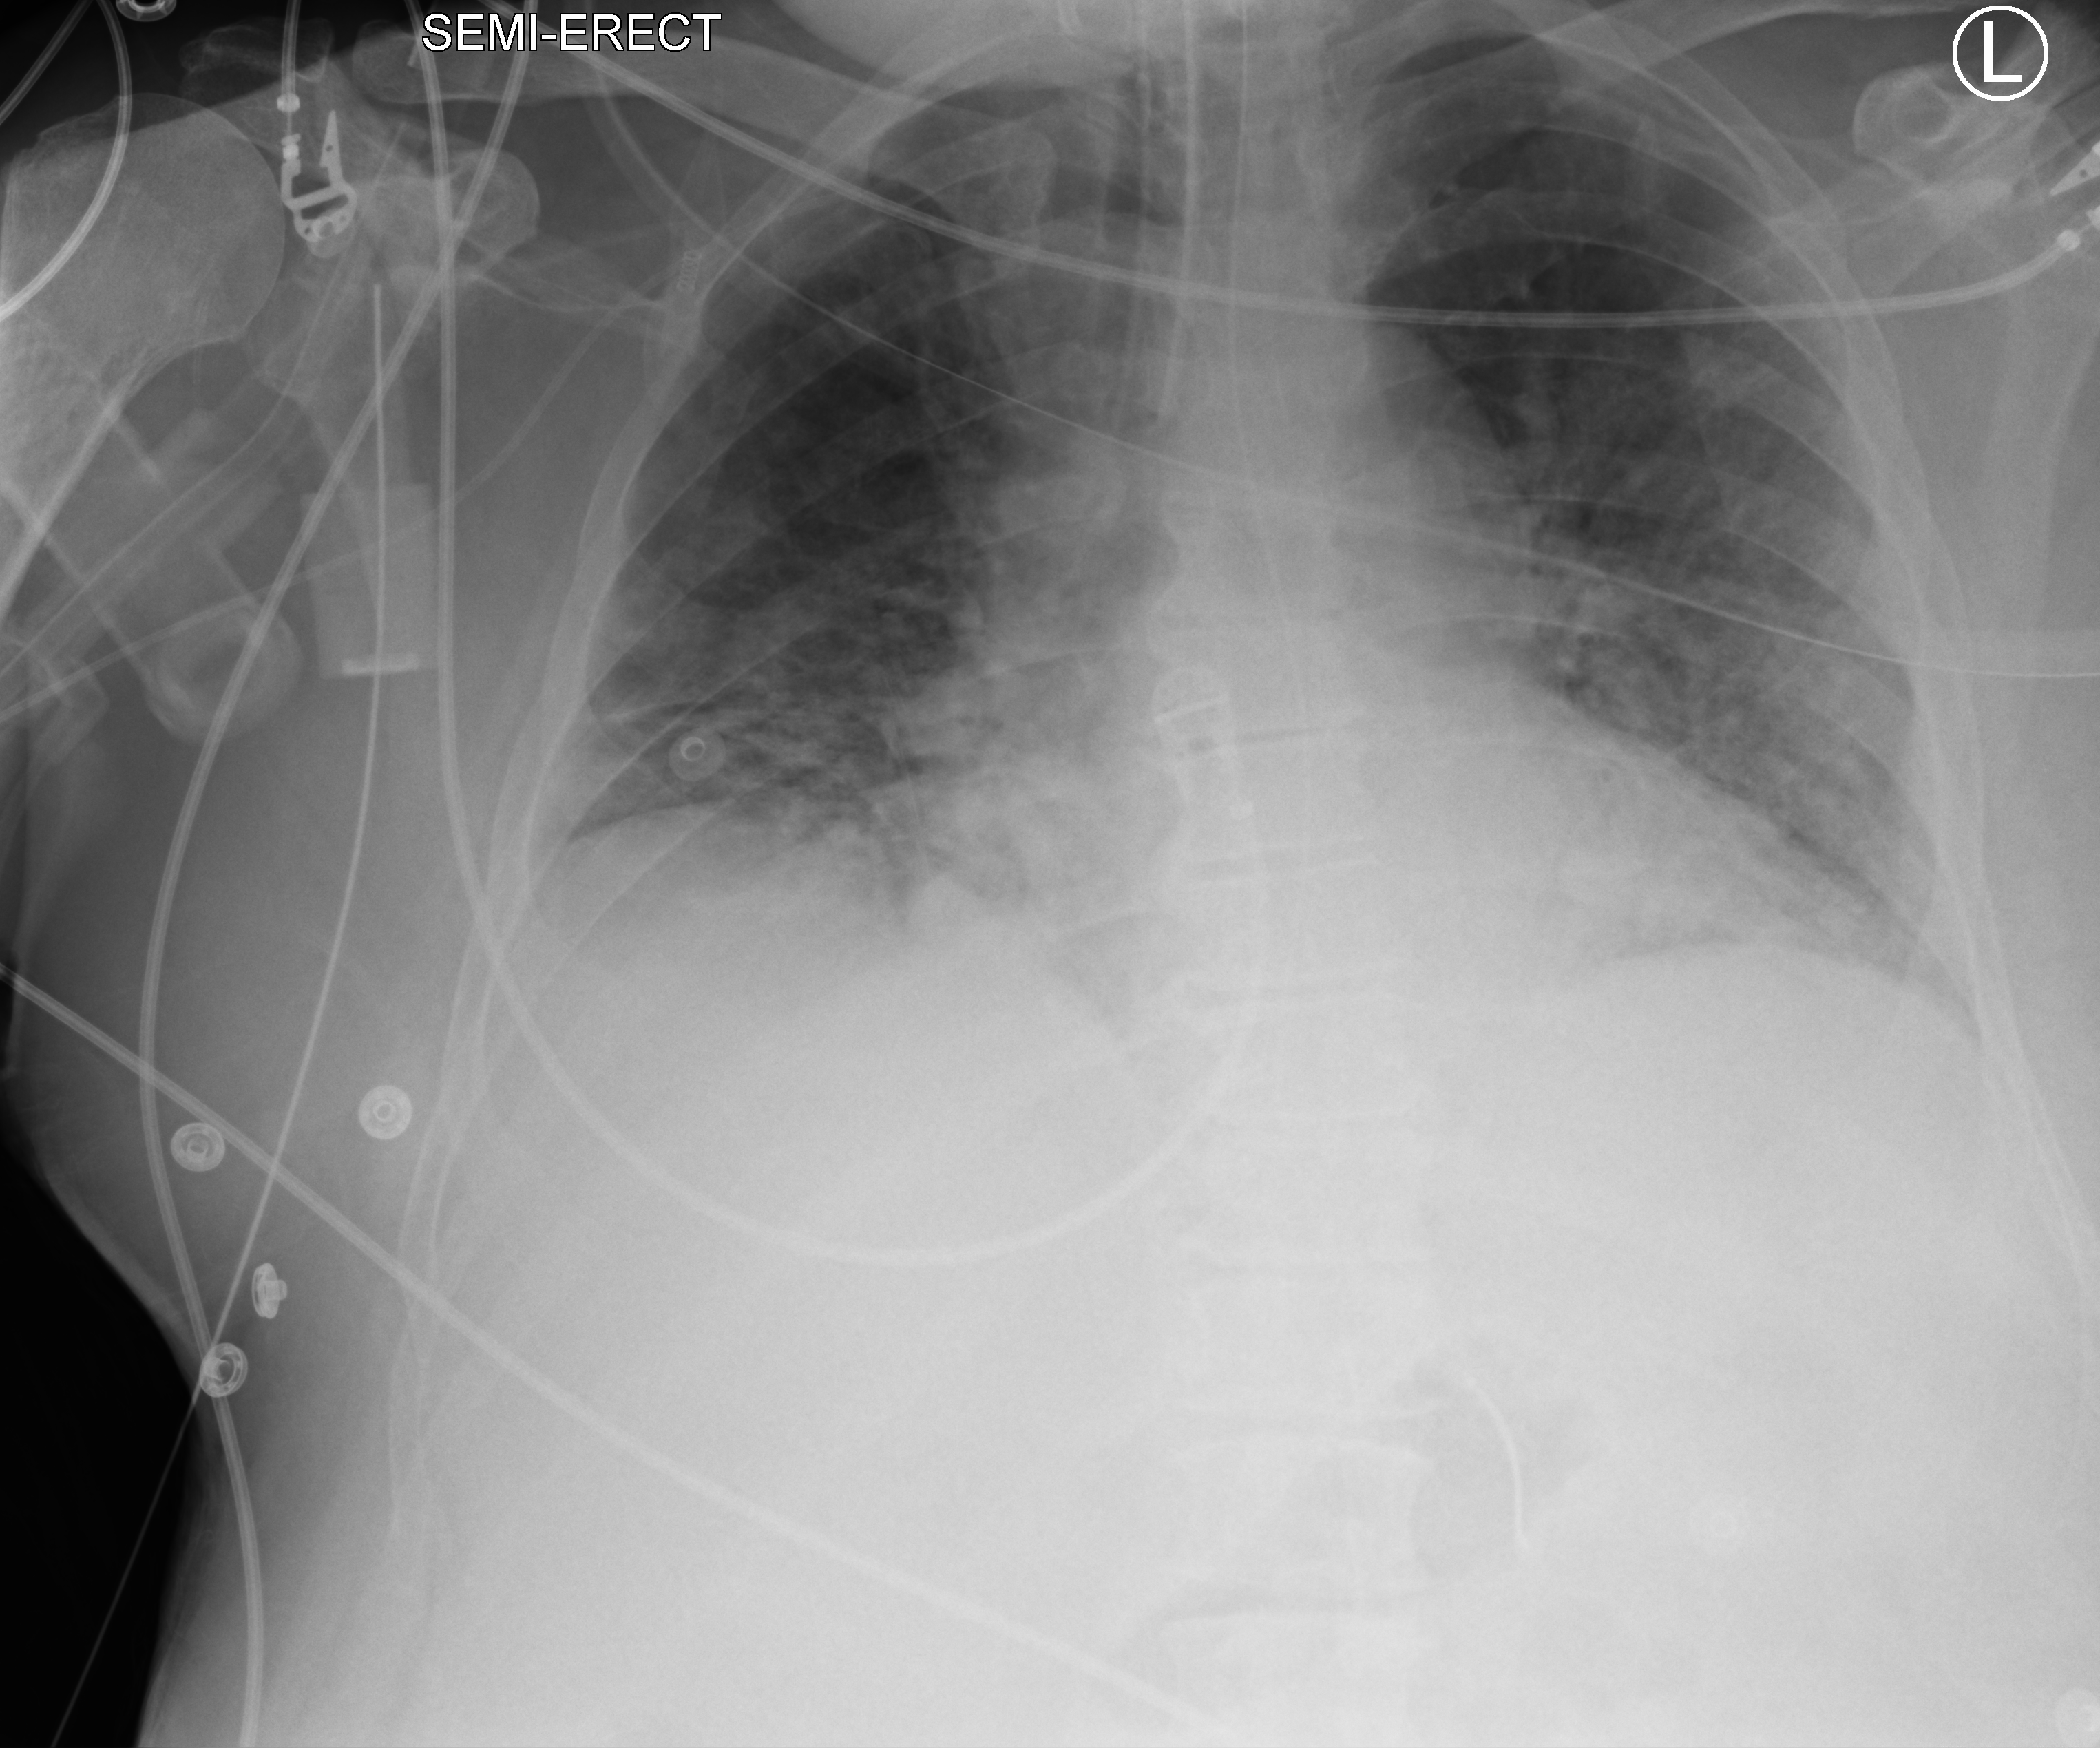
Bedside chest radiograph (computed radiography), anteroposterior (AP) projection. Male patient hospitalised with COVID-19, age 60–74 years.
Hospital-stay facts (about this admission, not read from this image; timing relative to this image not recorded): mechanically ventilated during this hospital stay: yes.